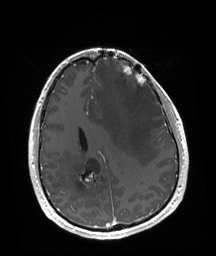
Brain MRI from a brain-tumour surgery series, one axial slice. Slice 66 of 192 in the series (ordered by position). T1-weighted post-contrast. 1 mm slice thickness. 216 × 256 image matrix. Case-level facts recorded for this patient, not image findings: tumour location: Left Frontal.
Structures marked on this image (expert manual segmentation):
- tumour: box from (x=122, y=66) to (x=146, y=88) px